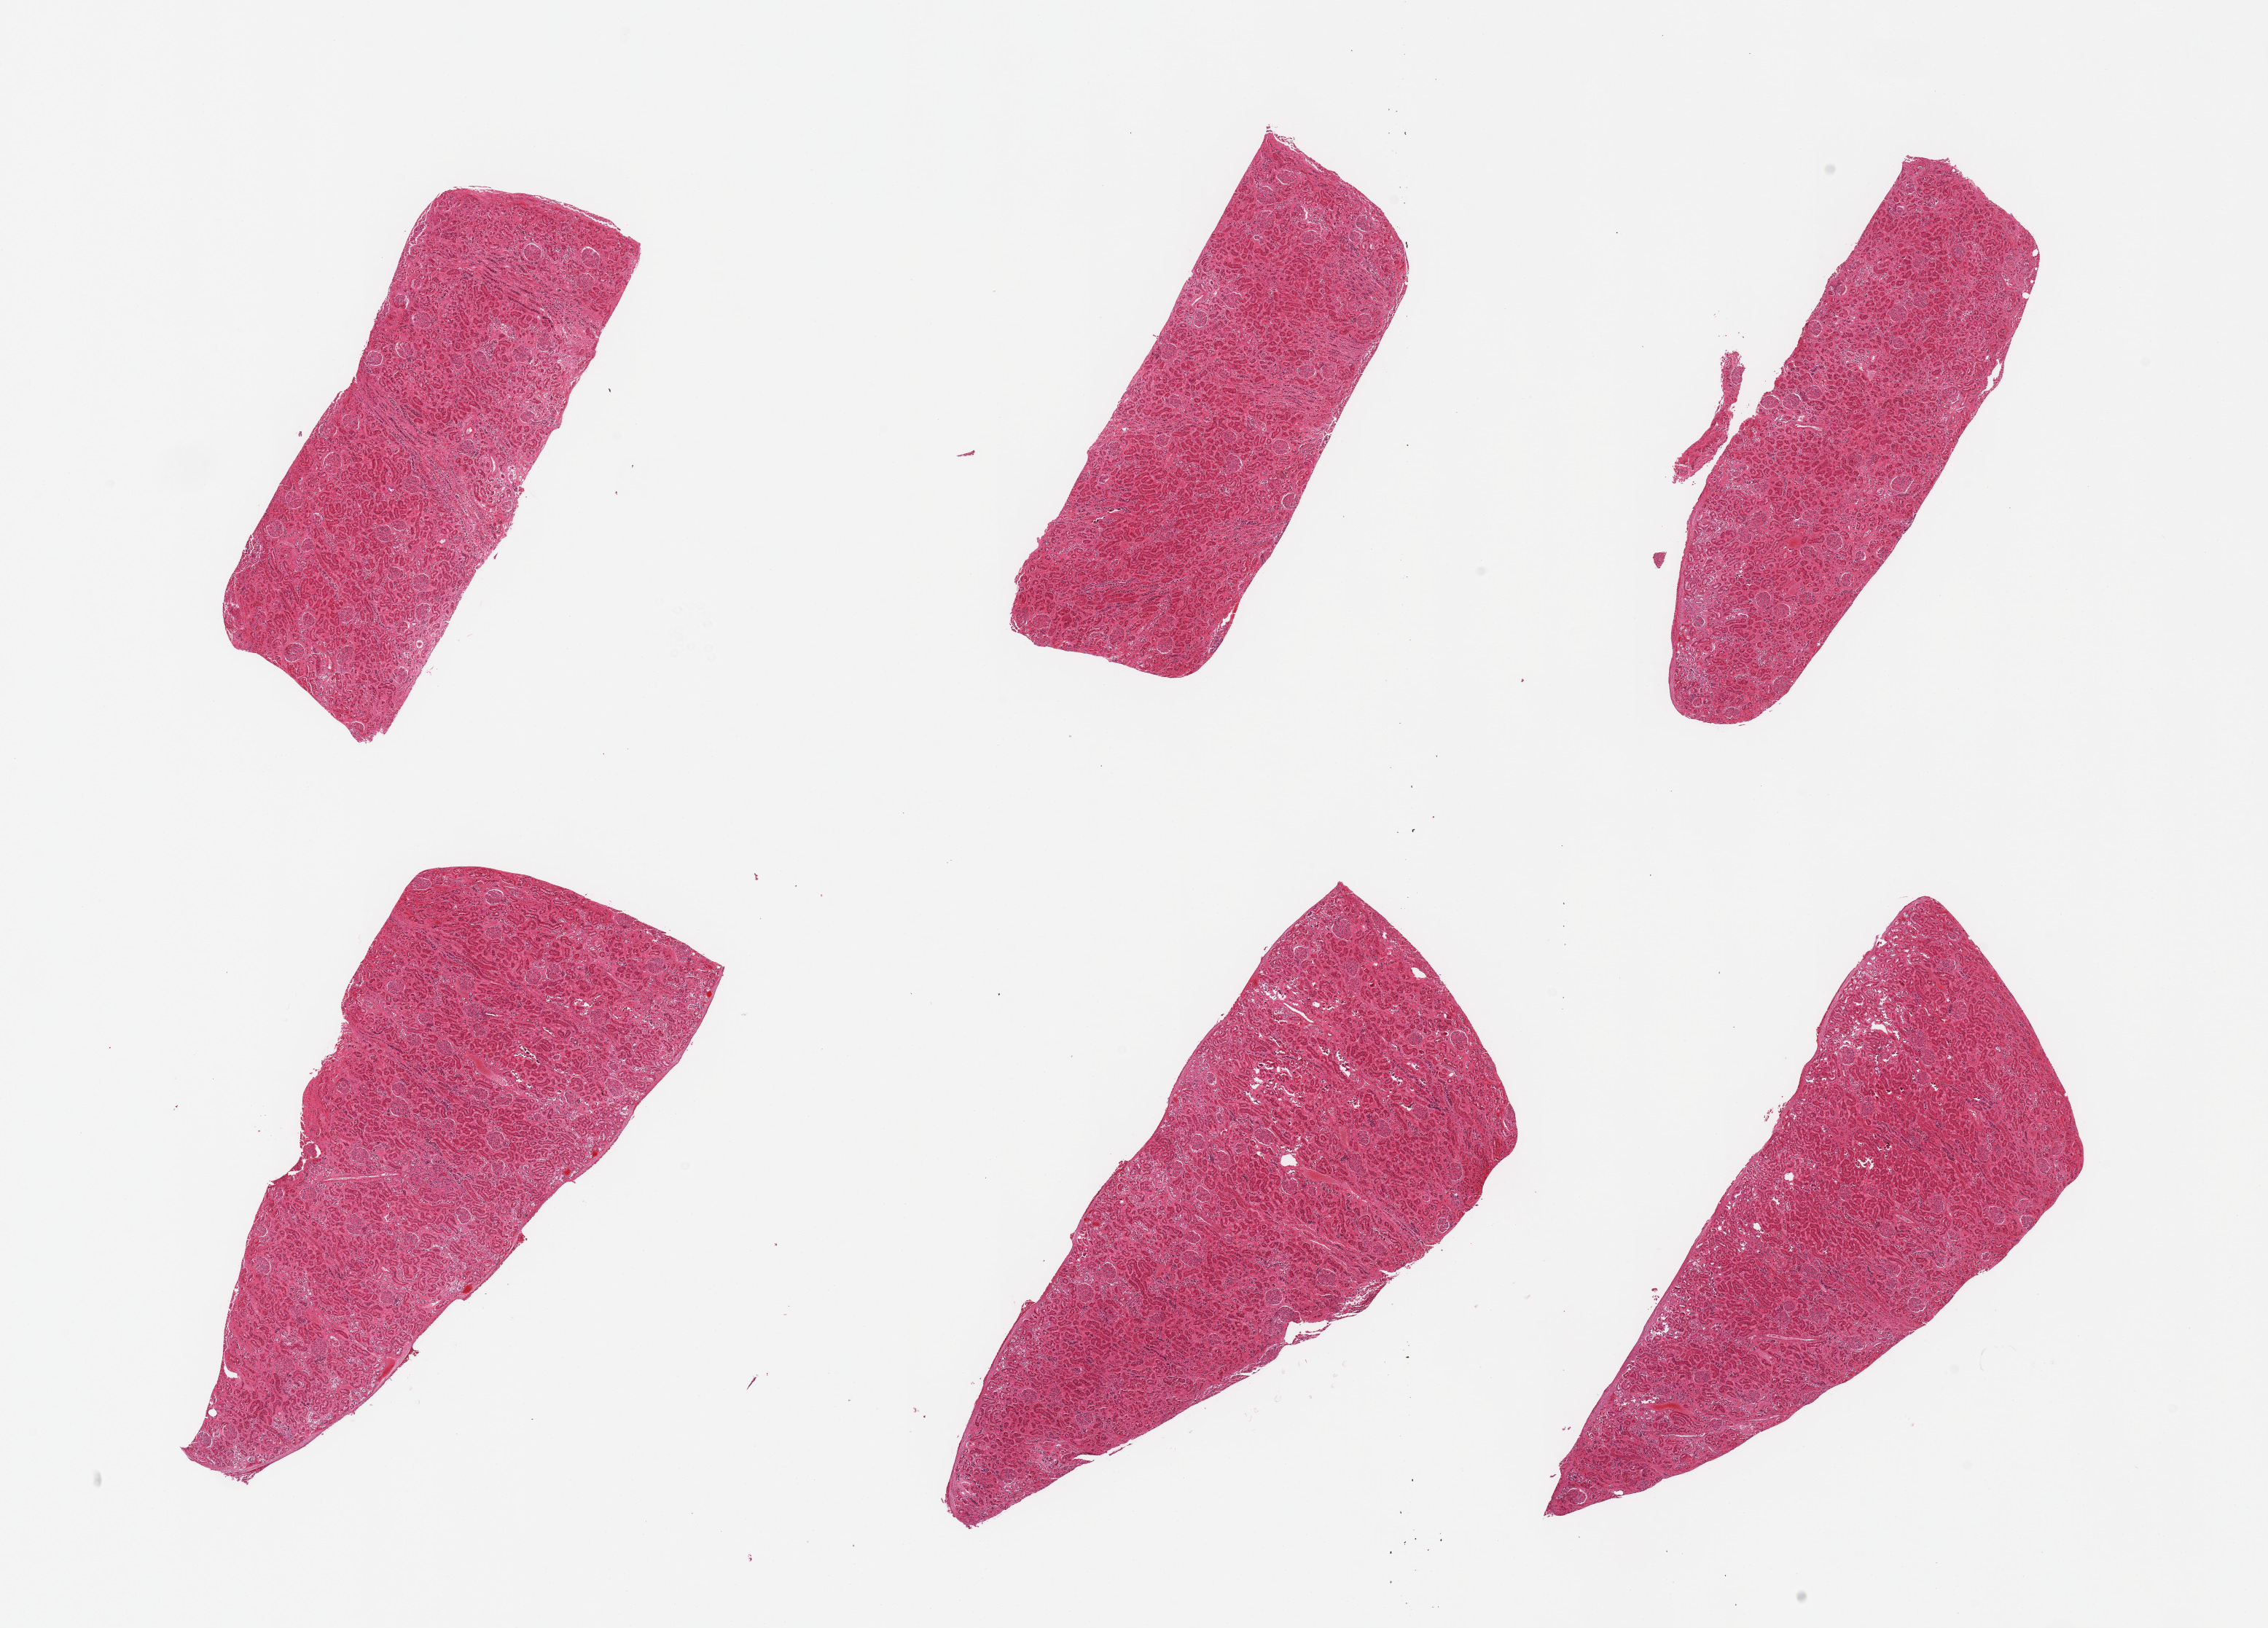
Digitized H&E-stained section — low-resolution overview of the scanned area, about 24.6 x 17.7 mm. PAXgene-fixed paraffin-embedded (PFPE) section. Target tissue: renal cortex. Donor tissue sample.
Review note (as recorded): 6 pieces, glomeruli present, tubules with advanced autolysis.